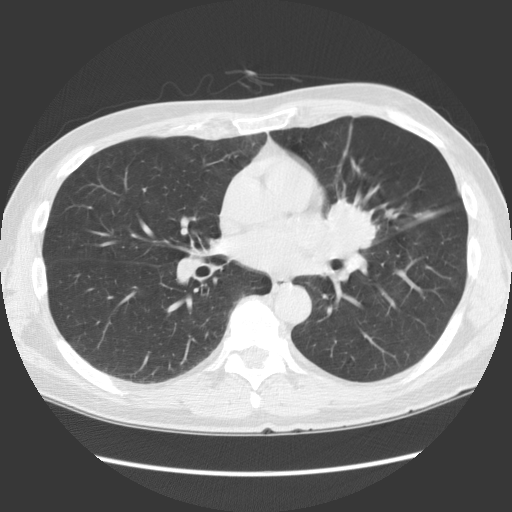
Chest CT (low-dose screening protocol), one axial image. Baseline screening round. Lung window (W 1500 / L -600 HU). 2.5 mm slice thickness. Male, age 61 years at enrolment. Former smoker at enrolment.
Expert reader's lesion annotation, bounding box <302,186,398,286> (left, top, right, bottom; pixels). Screening reader's record for this exam (one nodule recorded; not confirmed to be the boxed lesion): non-calcified nodule or mass ≥4 mm, lingula, 35 × 35 mm, spiculated (stellate) margins, soft tissue attenuation. Official screen result: positive, change unspecified: nodule(s) >= 4 mm or enlarging nodule(s), mass(es), or other non-specific abnormalities suspicious for lung cancer.